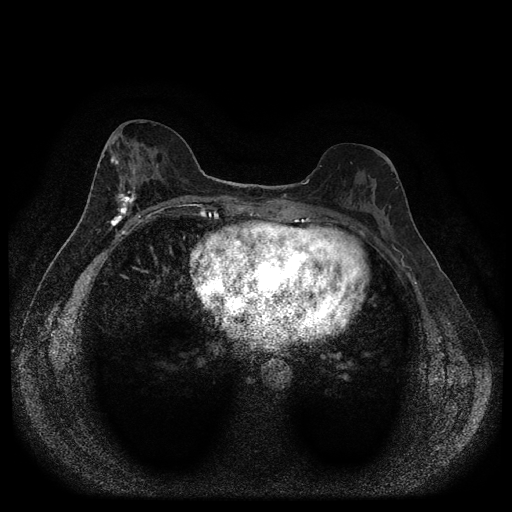
Breast MRI (dynamic contrast-enhanced, multi-phase), one axial slice; slice 44 of 116 in the series (ordered by position); dynamic contrast-enhanced series, time point 2 of 5 at this slice position (early post-contrast); 1.5 T; TE 2.7 ms, TR 5.4 ms; 512 × 512 image matrix. Female patient, age 49 years.
Annotated regions visible in this slice (semi-automatic segmentation, software-assisted and operator-edited):
- breast lesion (labelled 'tumour' in the annotation; benign lesions carry a separate 'benign' label): bounding box <107,155,140,231> (left, top, right, bottom; pixels)